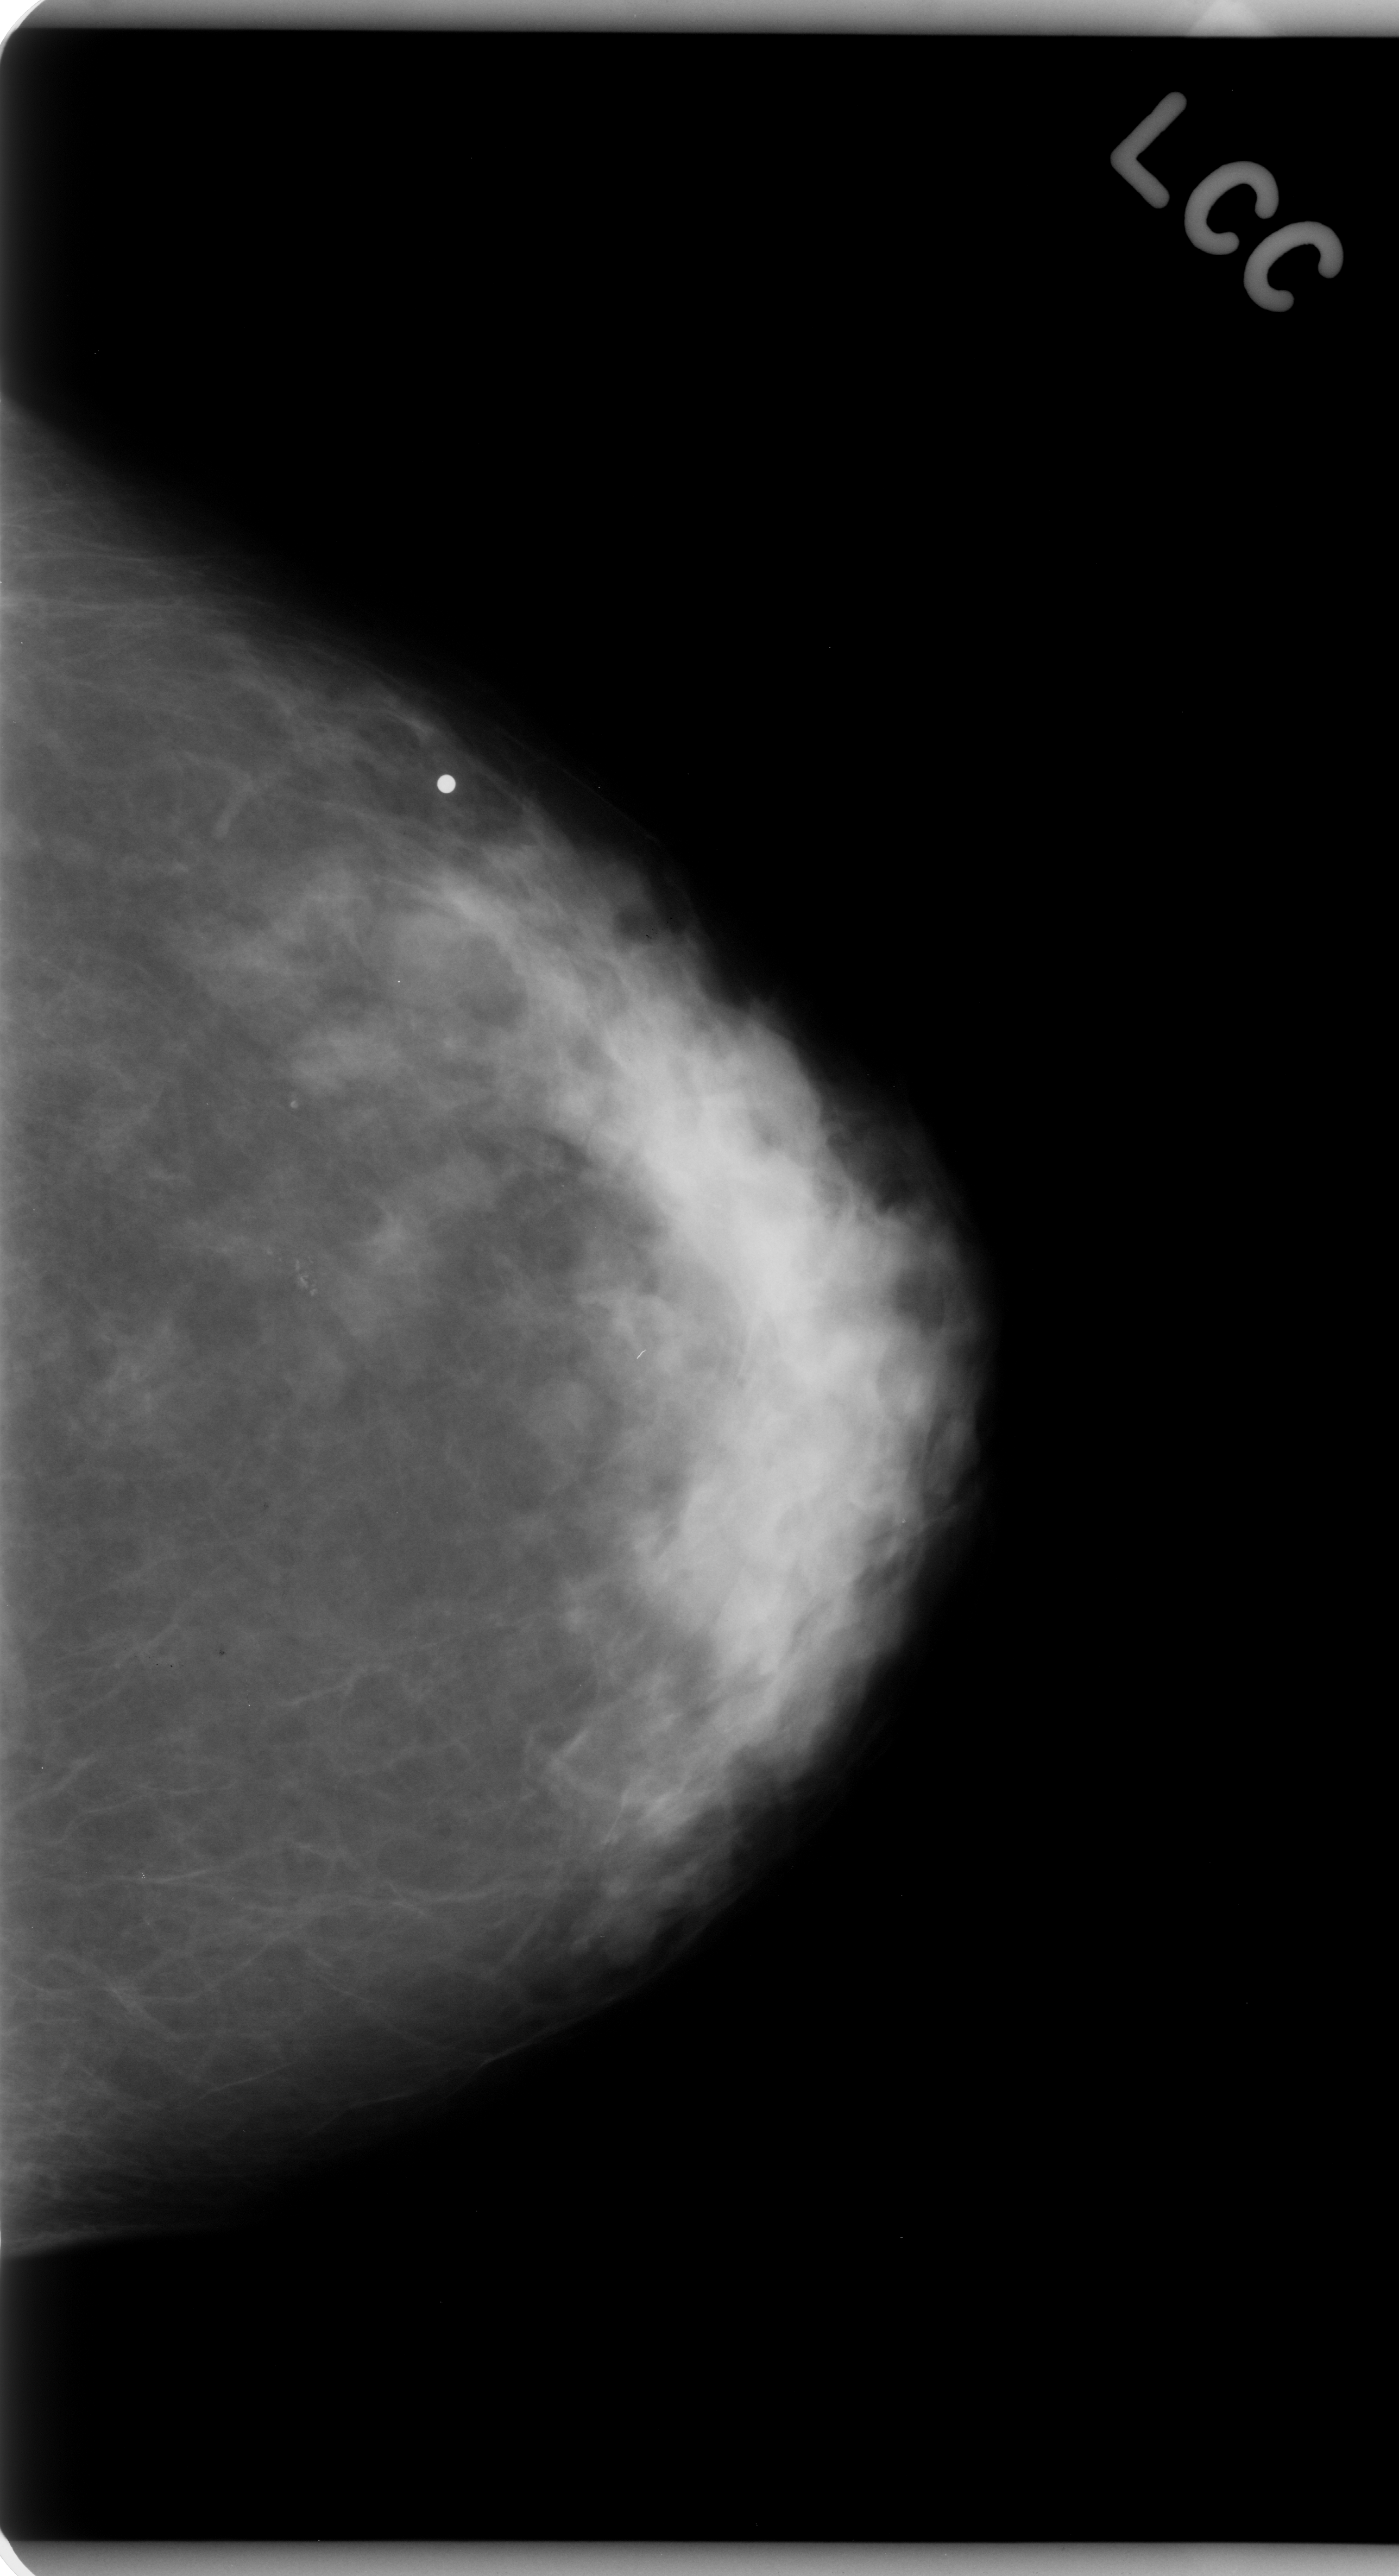
Digitized screen-film mammogram; left breast; craniocaudal (CC) view; BI-RADS breast density category 3 (scale 1–4).
Marked findings (only marked abnormalities are described; nothing is implied about the rest of the image): calcifications, morphology amorphous, distribution clustered; BI-RADS assessment category 4; subtlety rating 3 on a 1 (subtle) to 5 (obvious) scale; pathology result (as recorded, not read from the image): benign.